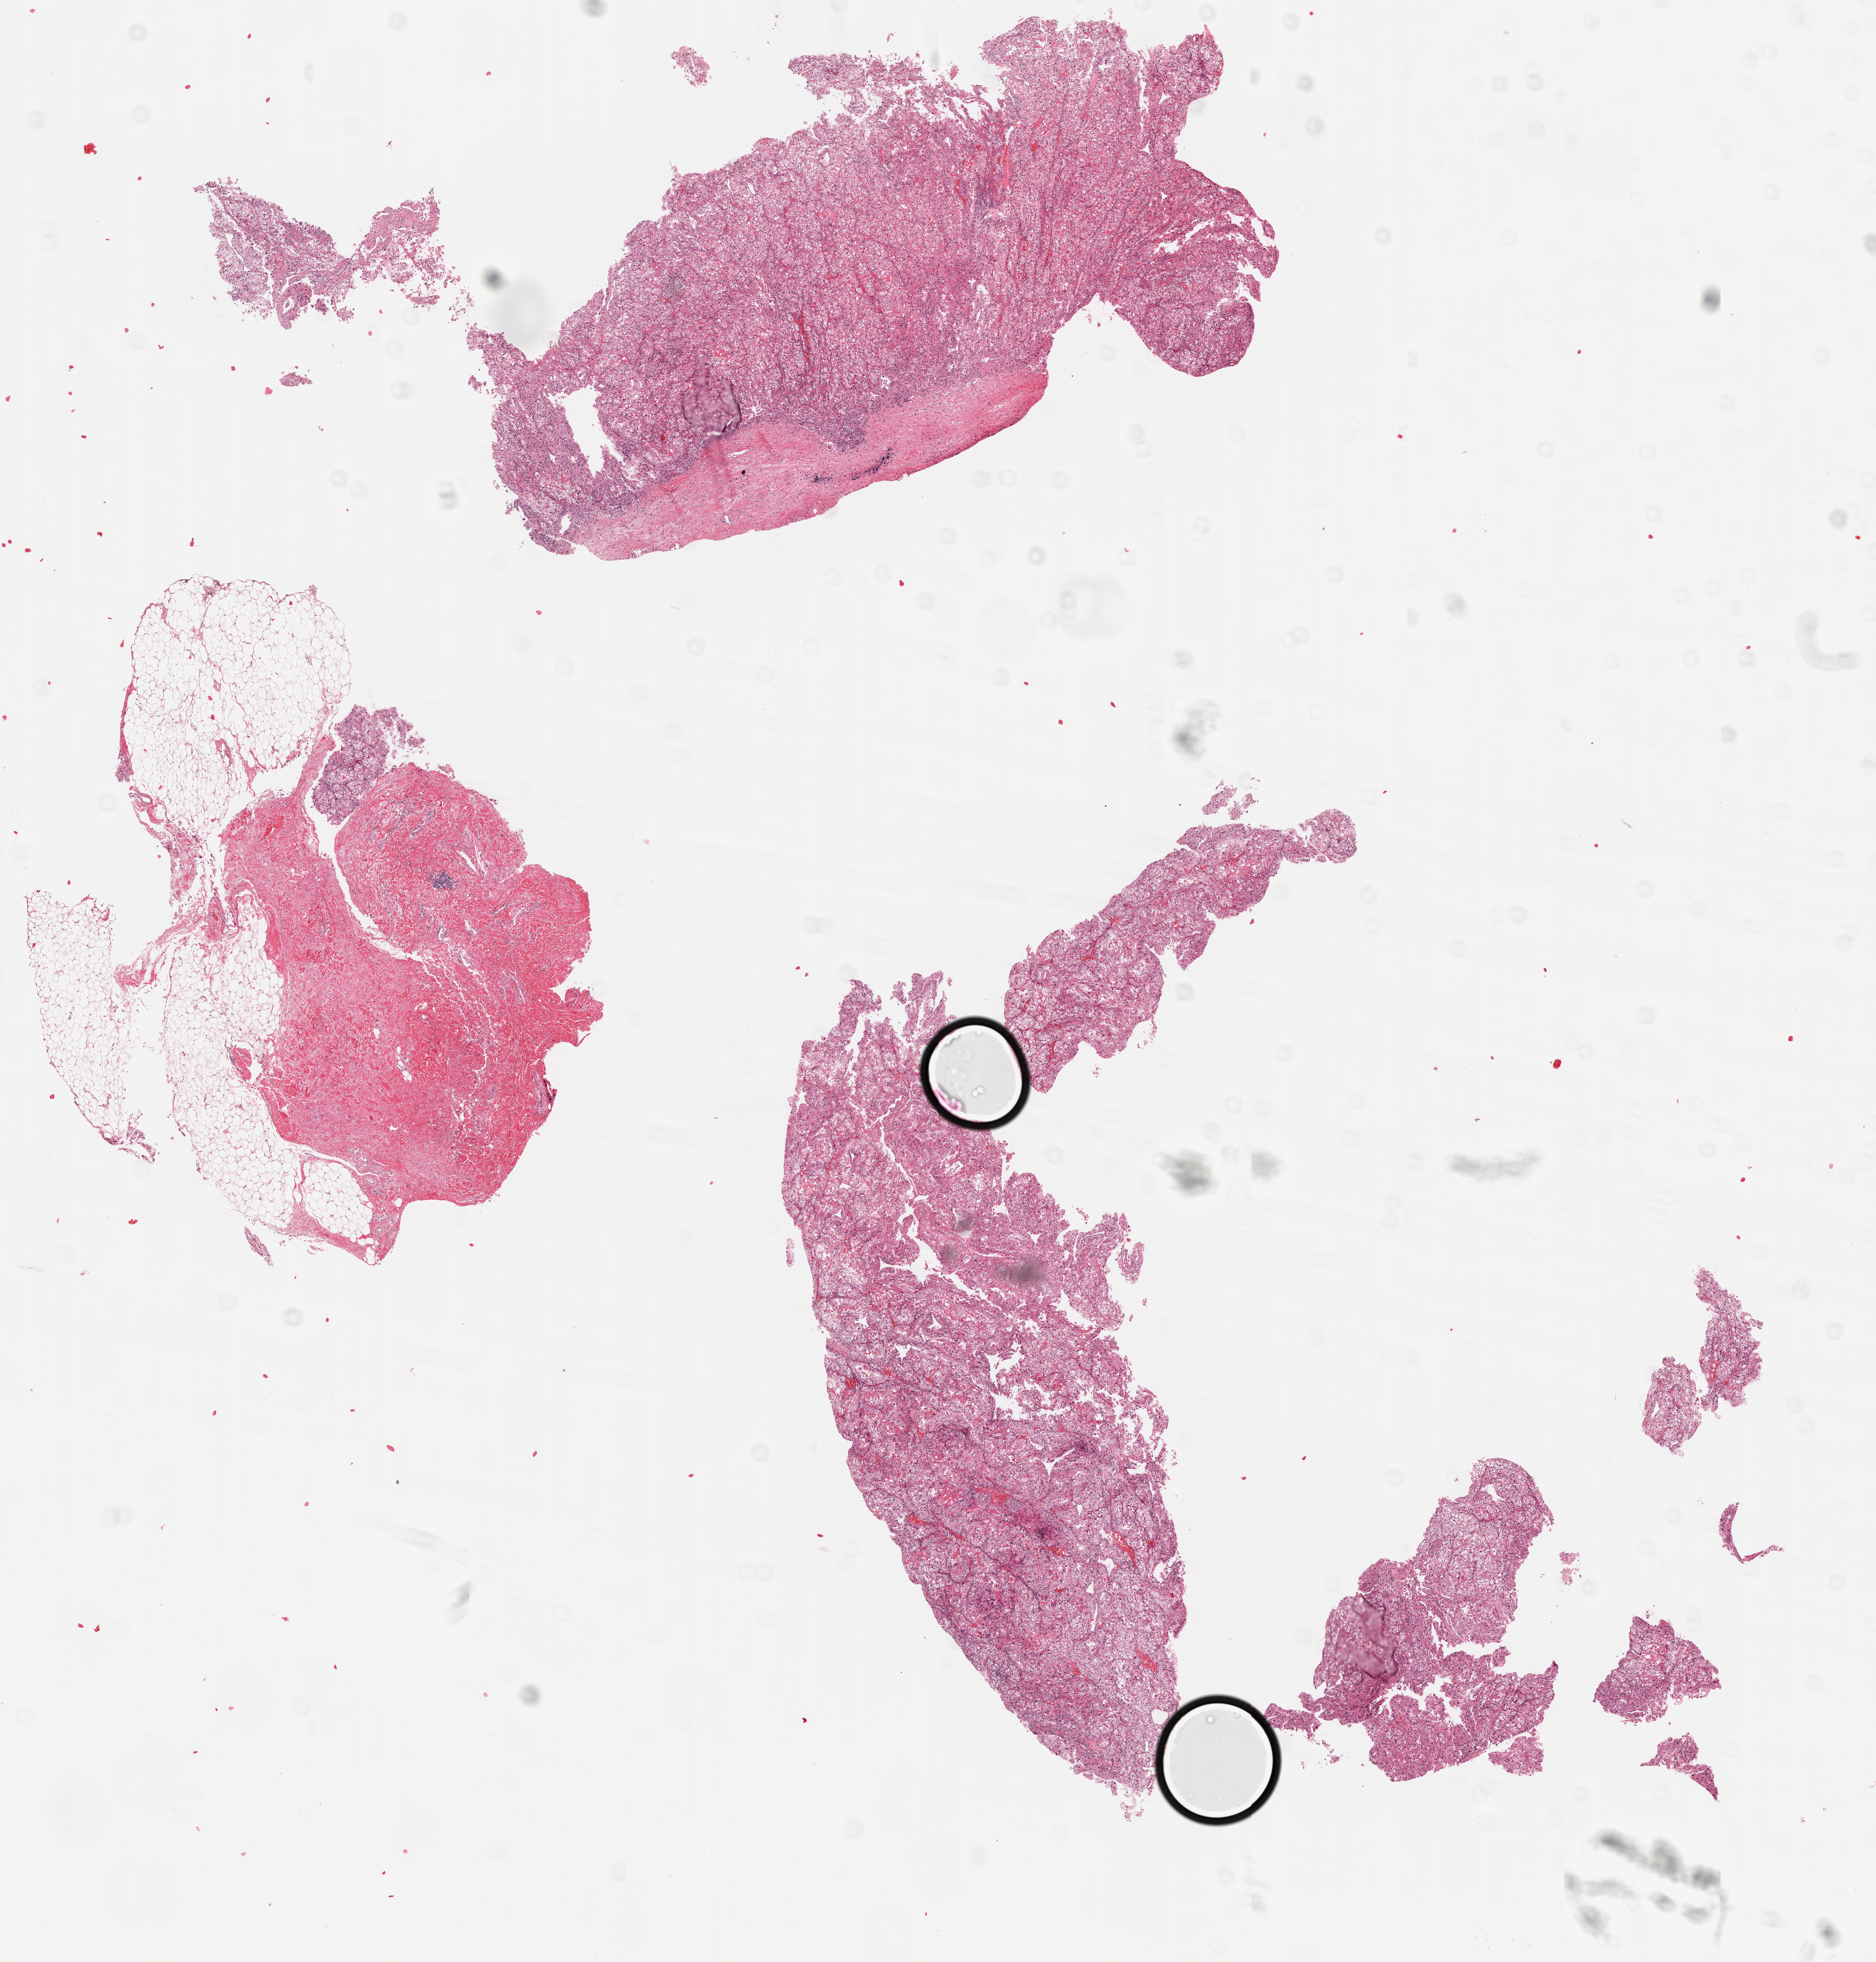
H&E-stained whole-slide image, low-resolution overview of the scanned area, about 11.9 x 12.4 mm. Tumour tissue sample, sampled site: kidney. Patient: male, age 41 years. Composition of this section per pathologist review: tumour nuclei 80%, necrosis 2%.
Diagnosis: Renal cell carcinoma, NOS.